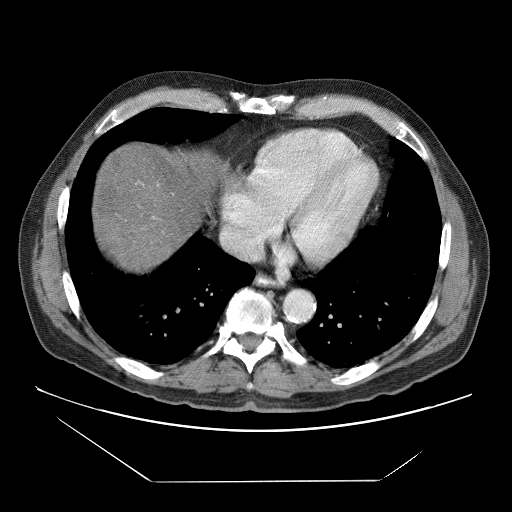
Contrast-enhanced abdominal CT (liver protocol), one axial slice. Slice 71 of 83 in the series (ordered by position). Reconstruction kernel STANDARD. Soft-tissue window (W 400 / L 40 HU). 2.5 mm slice thickness. 512 × 512 image matrix, field of view 420 × 420 mm. From the clinical record (not read from this slice): diagnosis: hepatocellular carcinoma (patient treated with transarterial chemoembolisation; whether this scan precedes or follows treatment is not stated here); TNM stage (as recorded): Stage-IVB; Child-Pugh class: B.
Outlined on this slice (semi-automatically segmented with operator editing):
- abdominal aorta: box from (x=285, y=291) to (x=314, y=320) px
- liver parenchyma outside the tumour (the mass and vessels are separate outlines, so this box may not span the whole liver): (x=94, y=142)–(x=226, y=268)